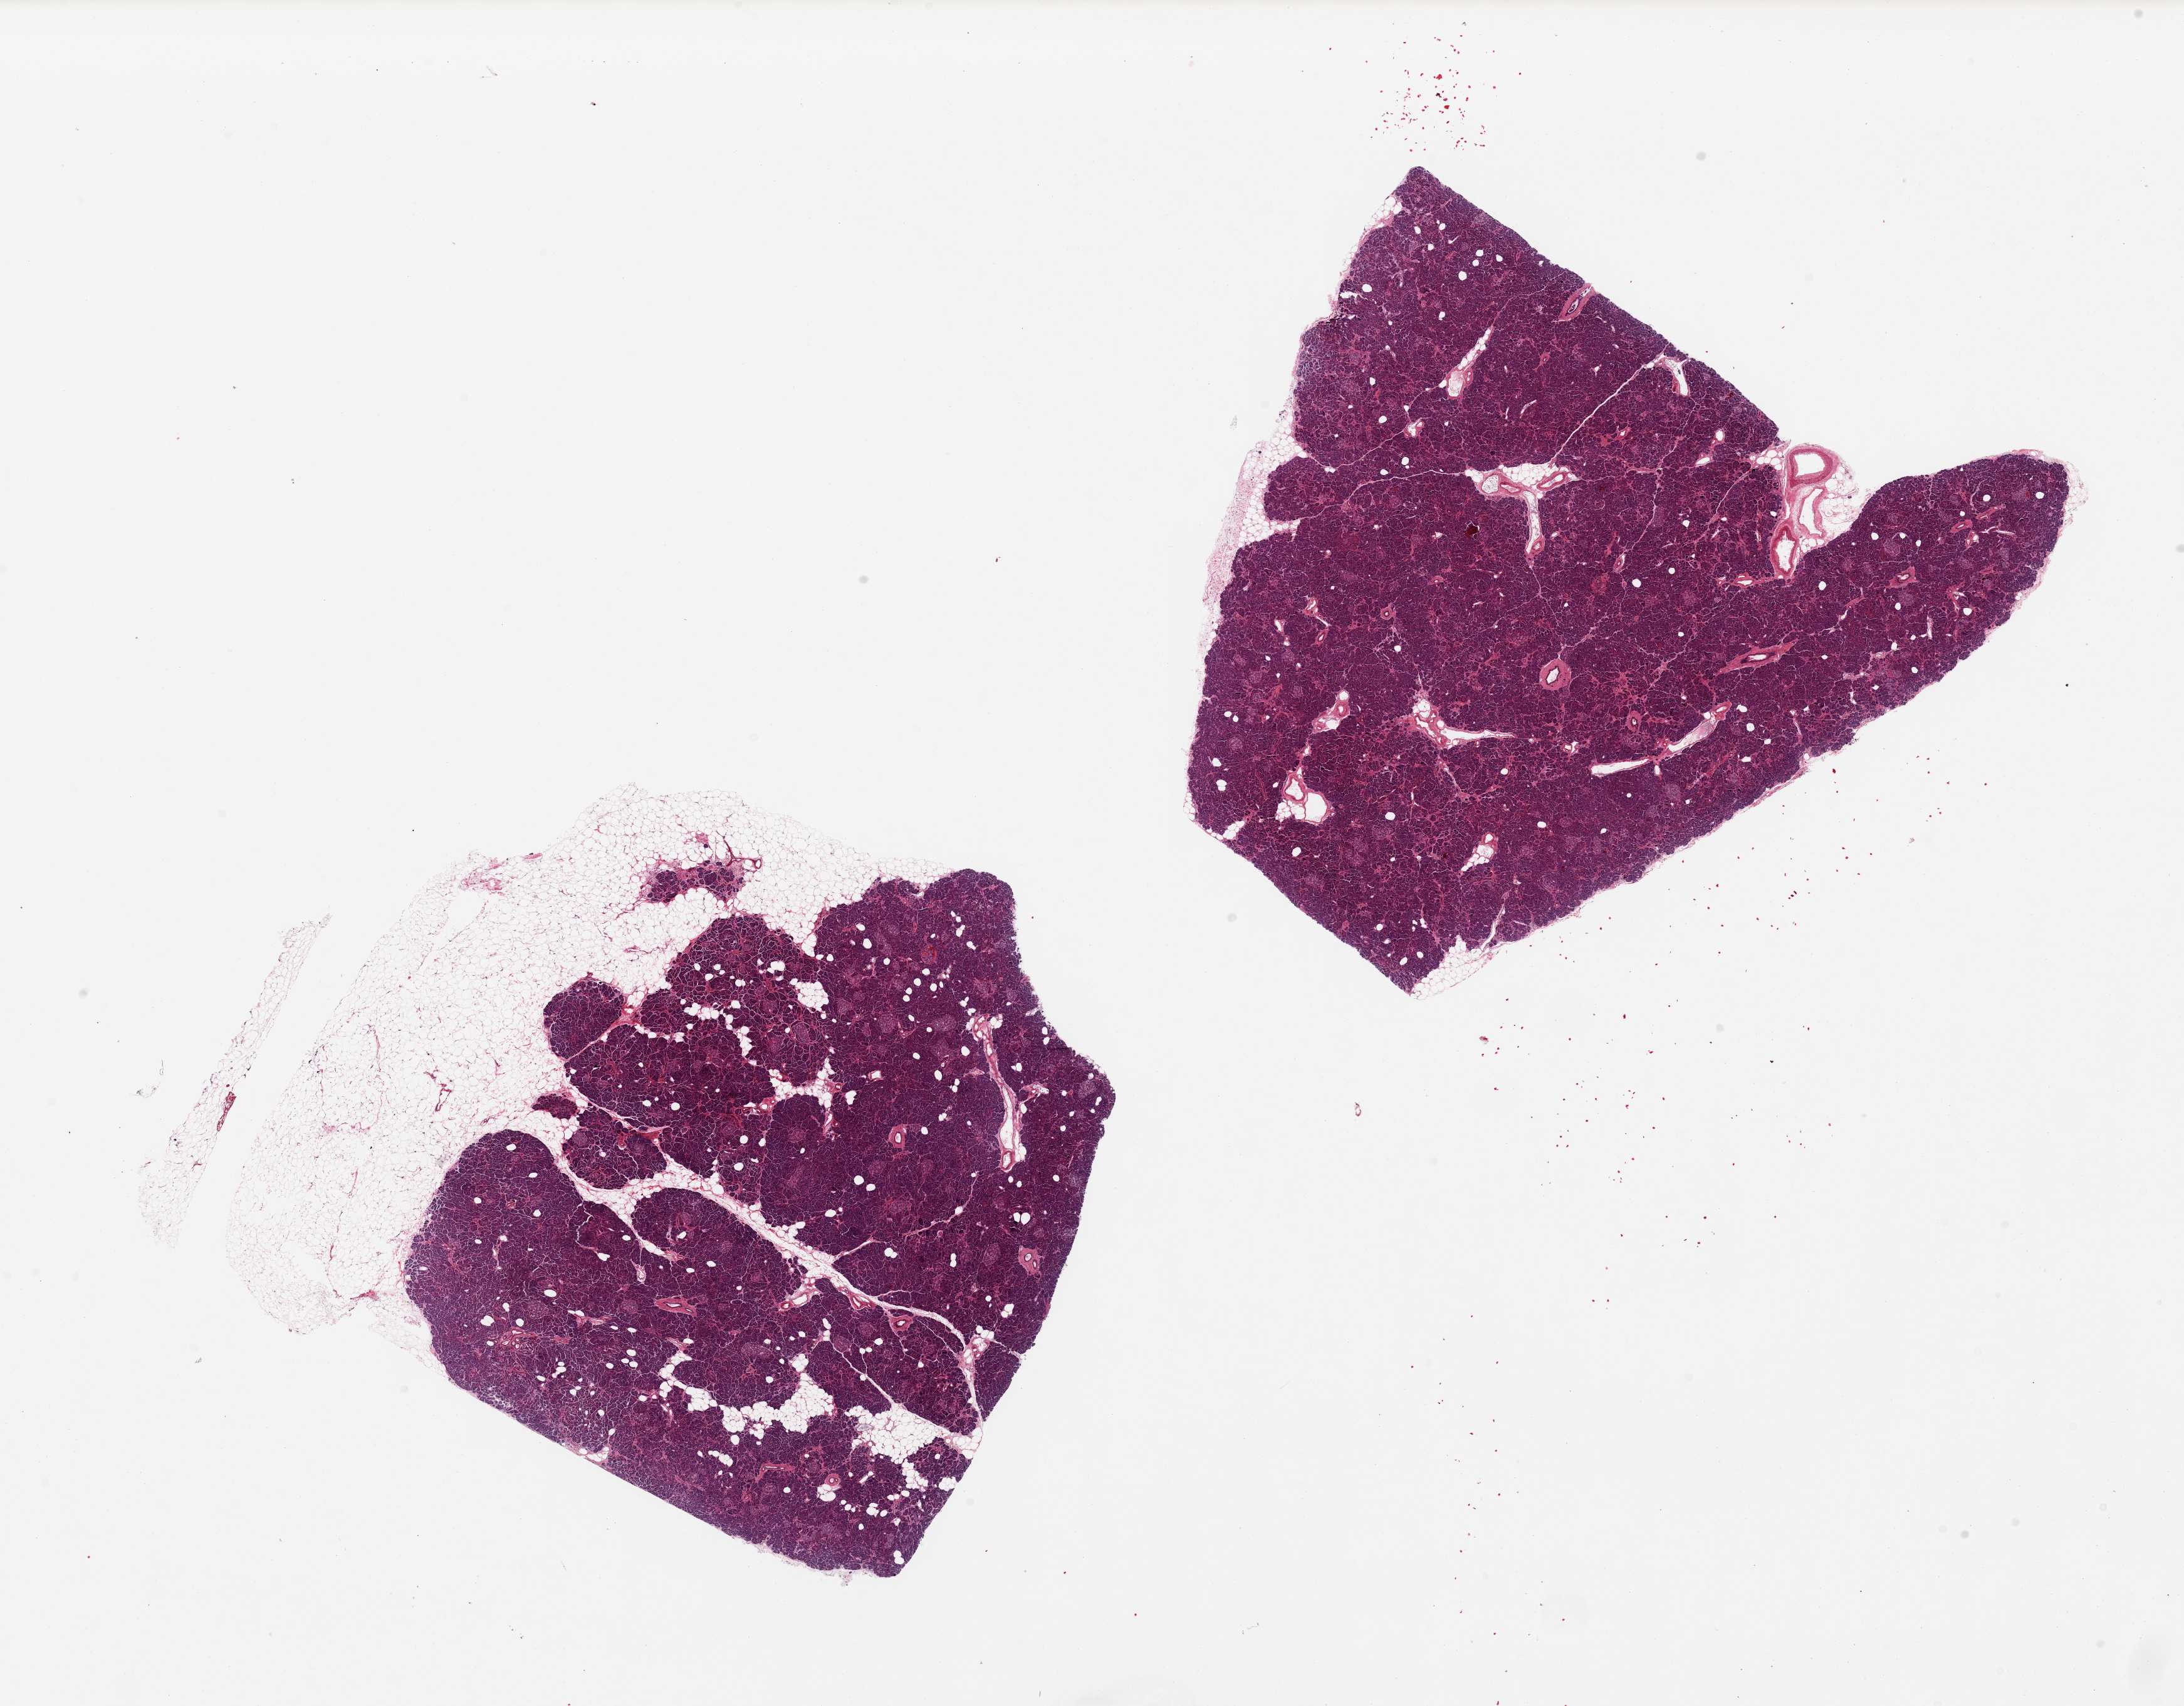
Digitized H&E-stained section — whole scanned area (about 27.6 x 21.5 mm, acquisition: 20x scan) shown as a low-resolution overview, PAXgene-fixed paraffin-embedded (PFPE) section, section of pancreas (target tissue), tissue donor sample. Donor: female.
* review note (as recorded): 2 pieces, well - preserved; Islets-well visualized; Adherent ~2mm fatty aggregated on one section